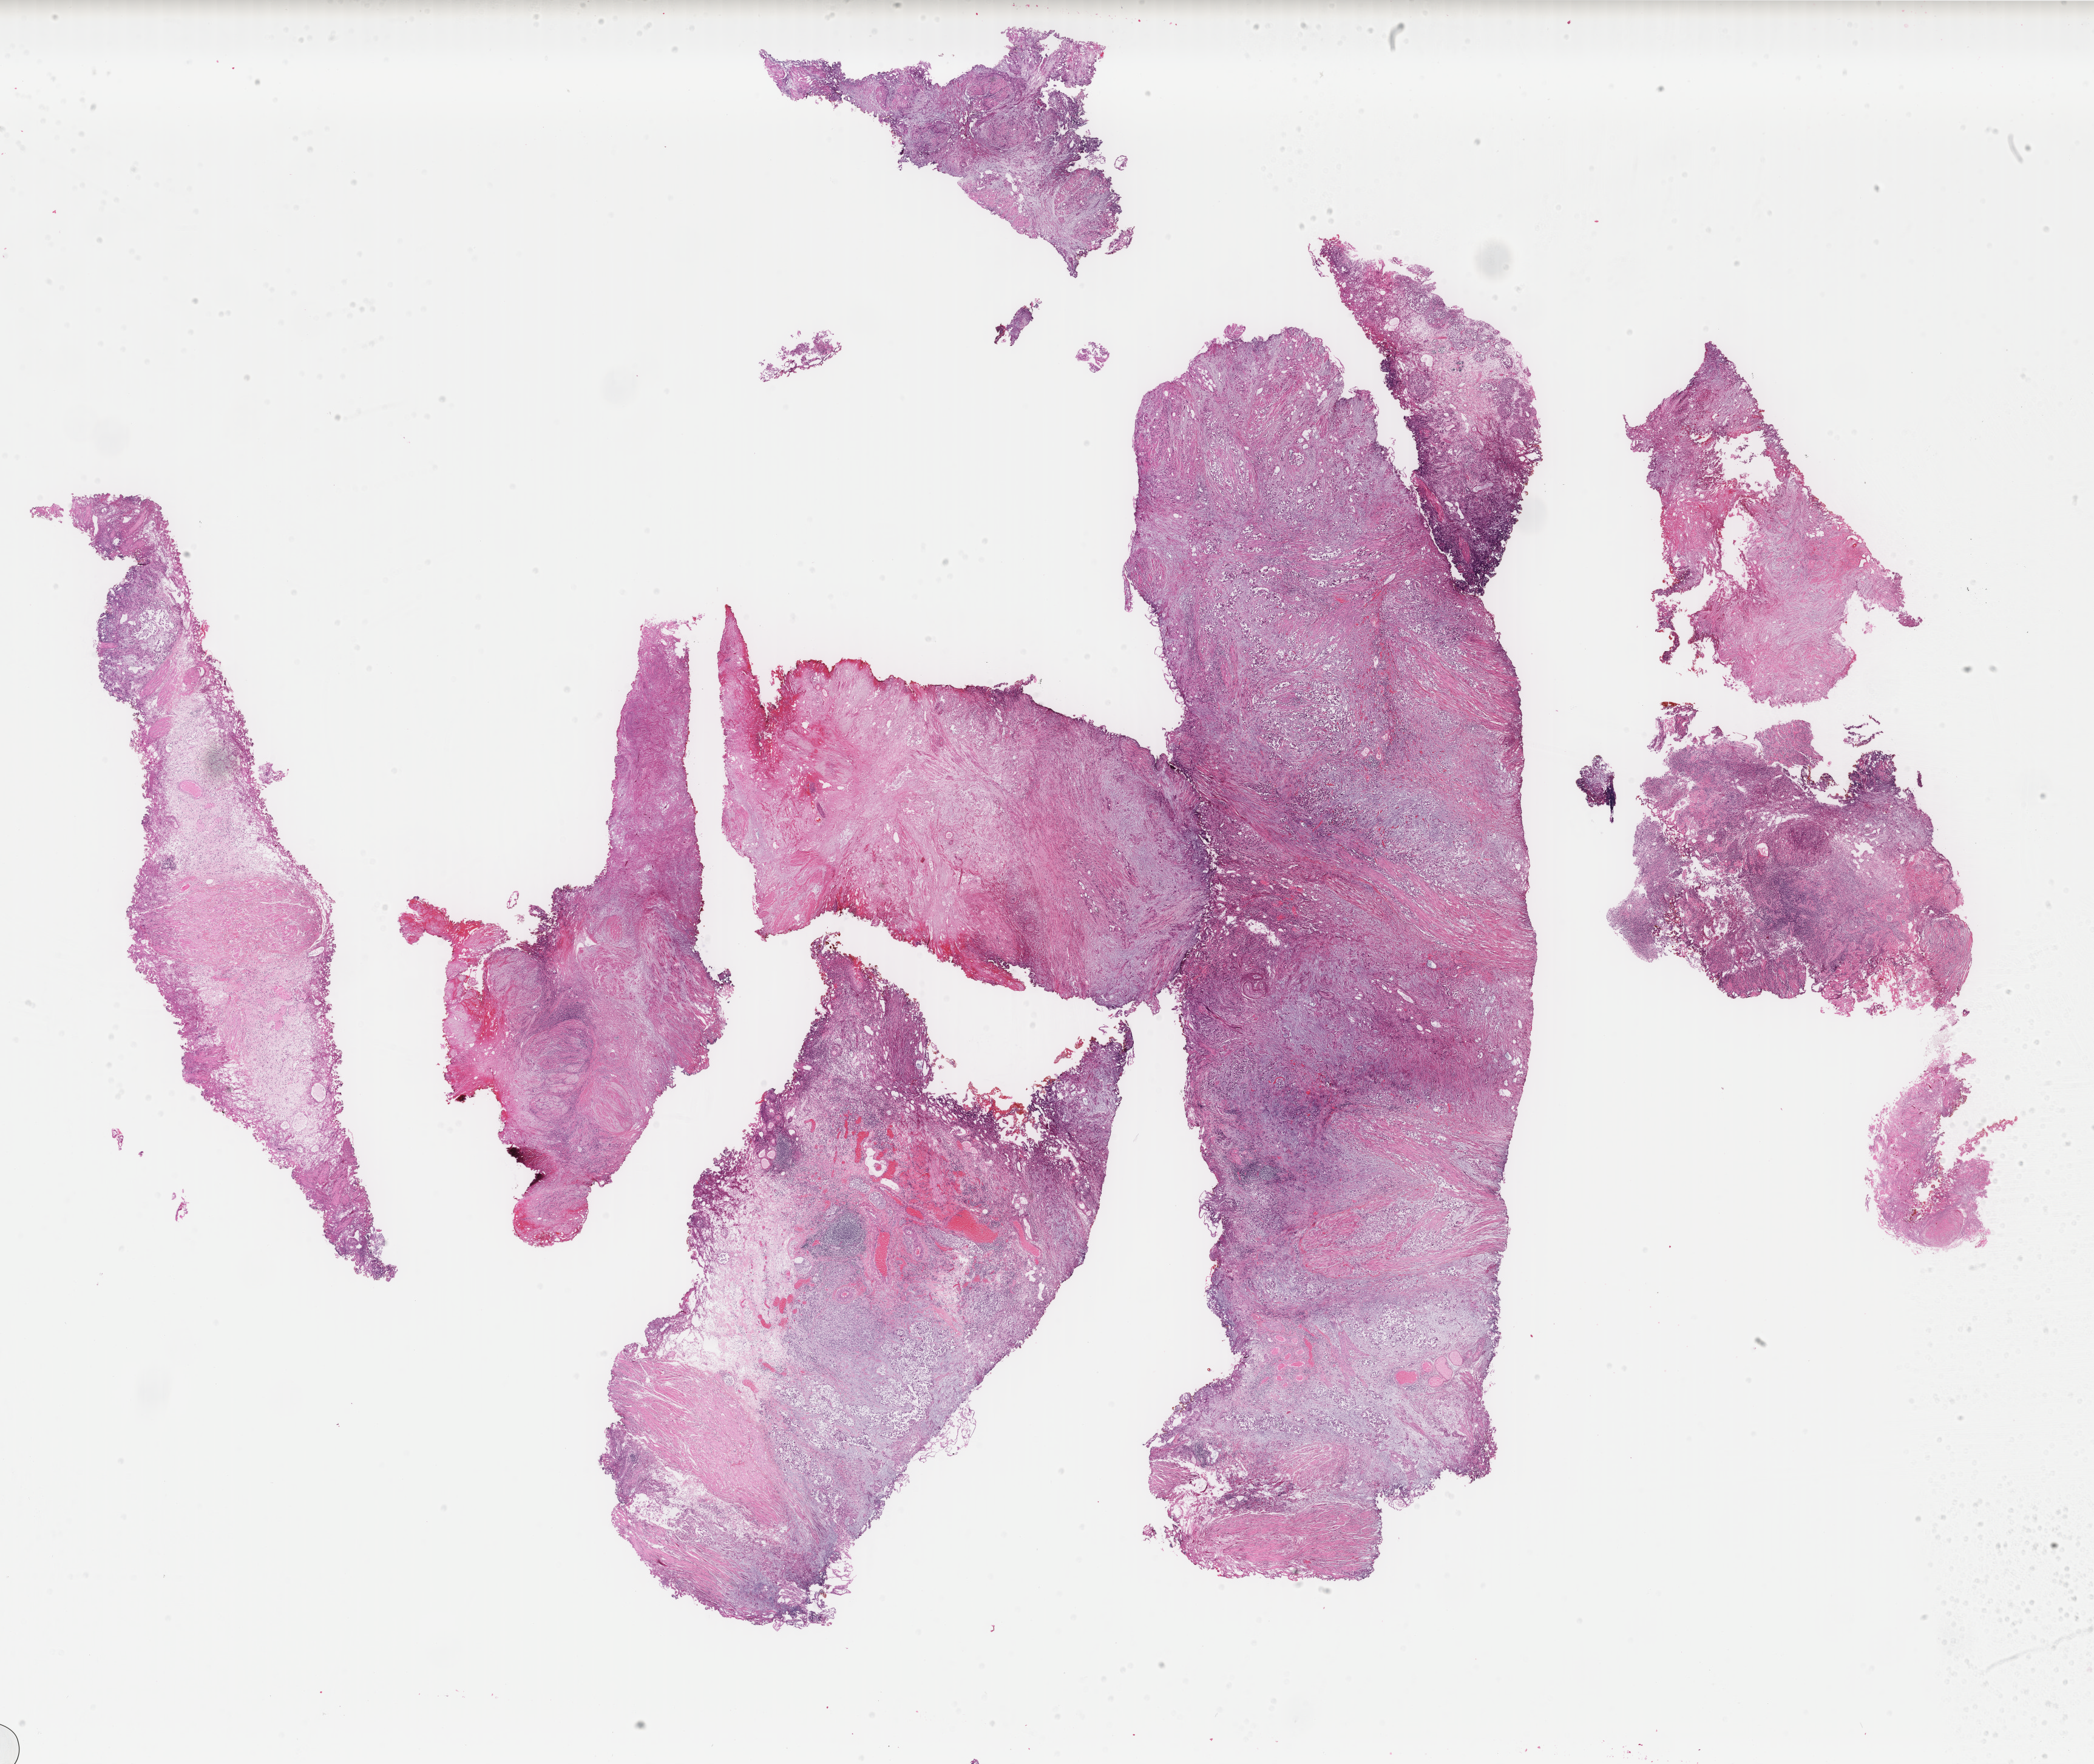
Digitized Hematoxylin and eosin (H&E) stained tissue section (whole slide) — a low-resolution overview of the entire scanned area, about 27.4 x 23.1 mm; formalin-fixed paraffin-embedded (FFPE) diagnostic section; bladder, primary tumour sample. Female, age 58 years at initial diagnosis.
Pathologic diagnosis: Transitional cell carcinoma.